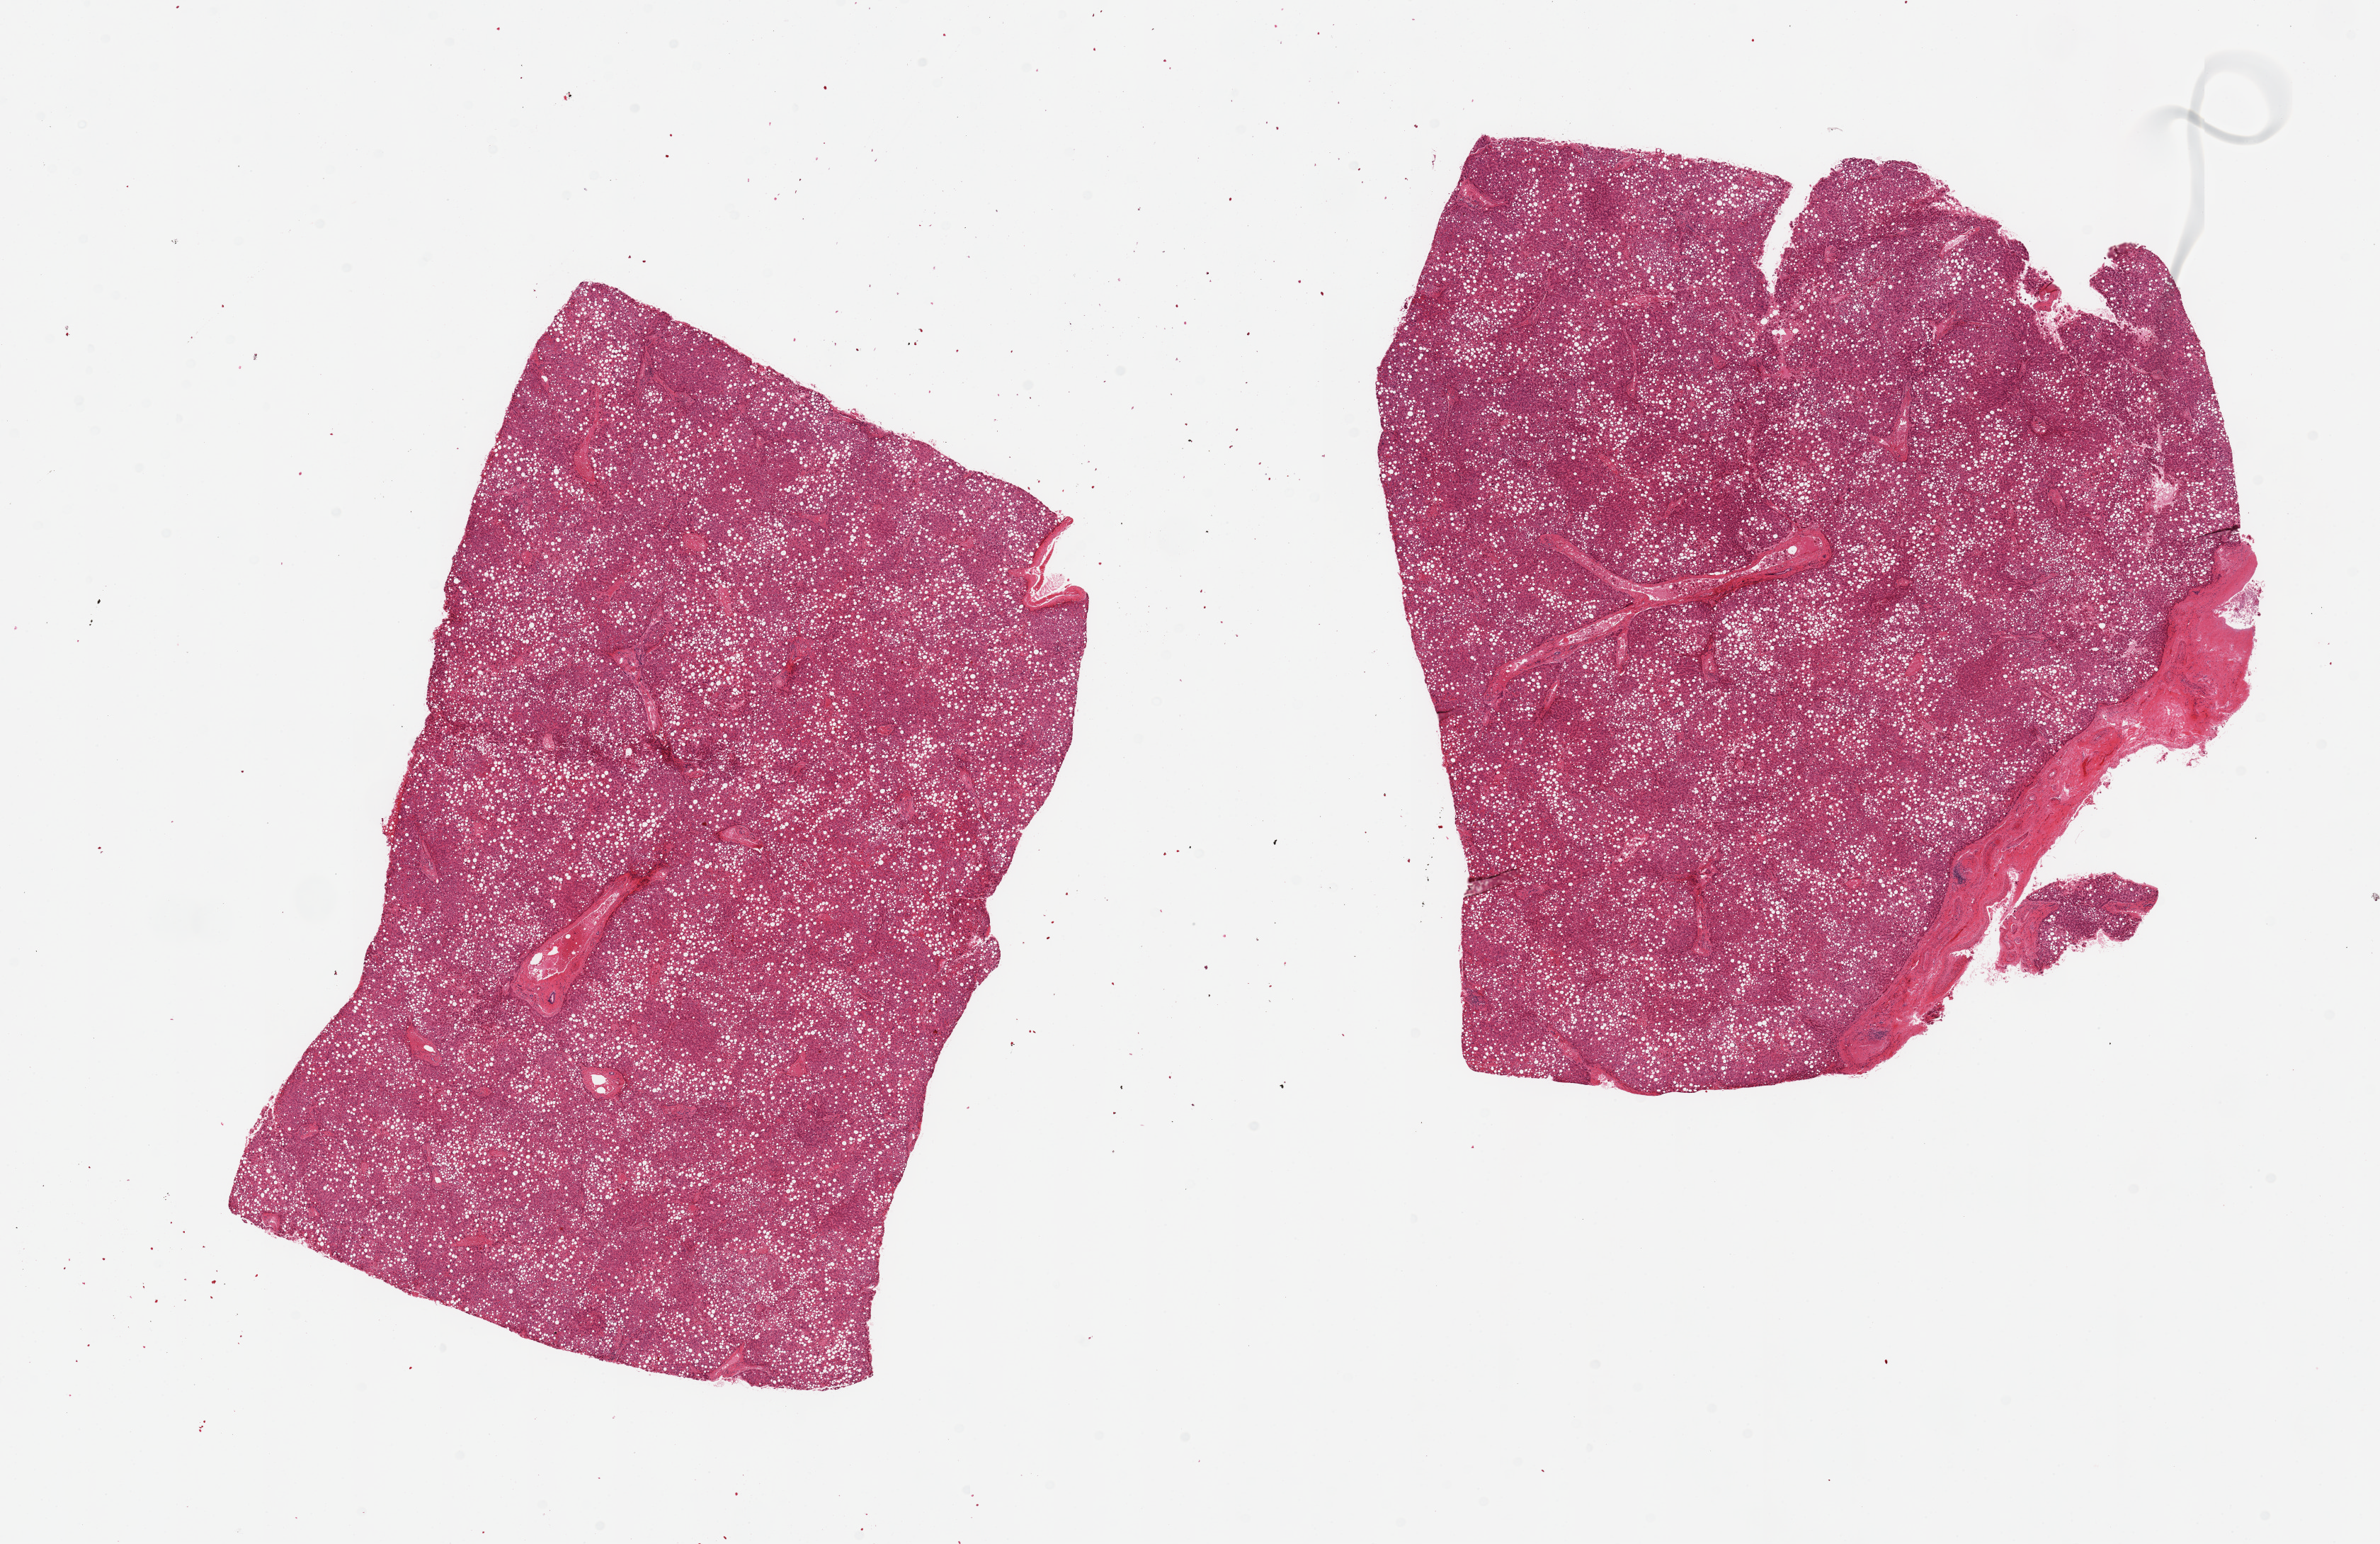
Digitized H&E-stained section — whole scanned area (about 26.6 x 17.2 mm, acquisition: 20x scan) shown as a low-resolution overview. PAXgene-fixed paraffin-embedded (PFPE) section. Sampled site (target tissue): liver. Donor tissue sample. Male donor.
* pathologist's review note for this sample: 2 pieces; moderate macrovesicular steatosis with some fibrosis